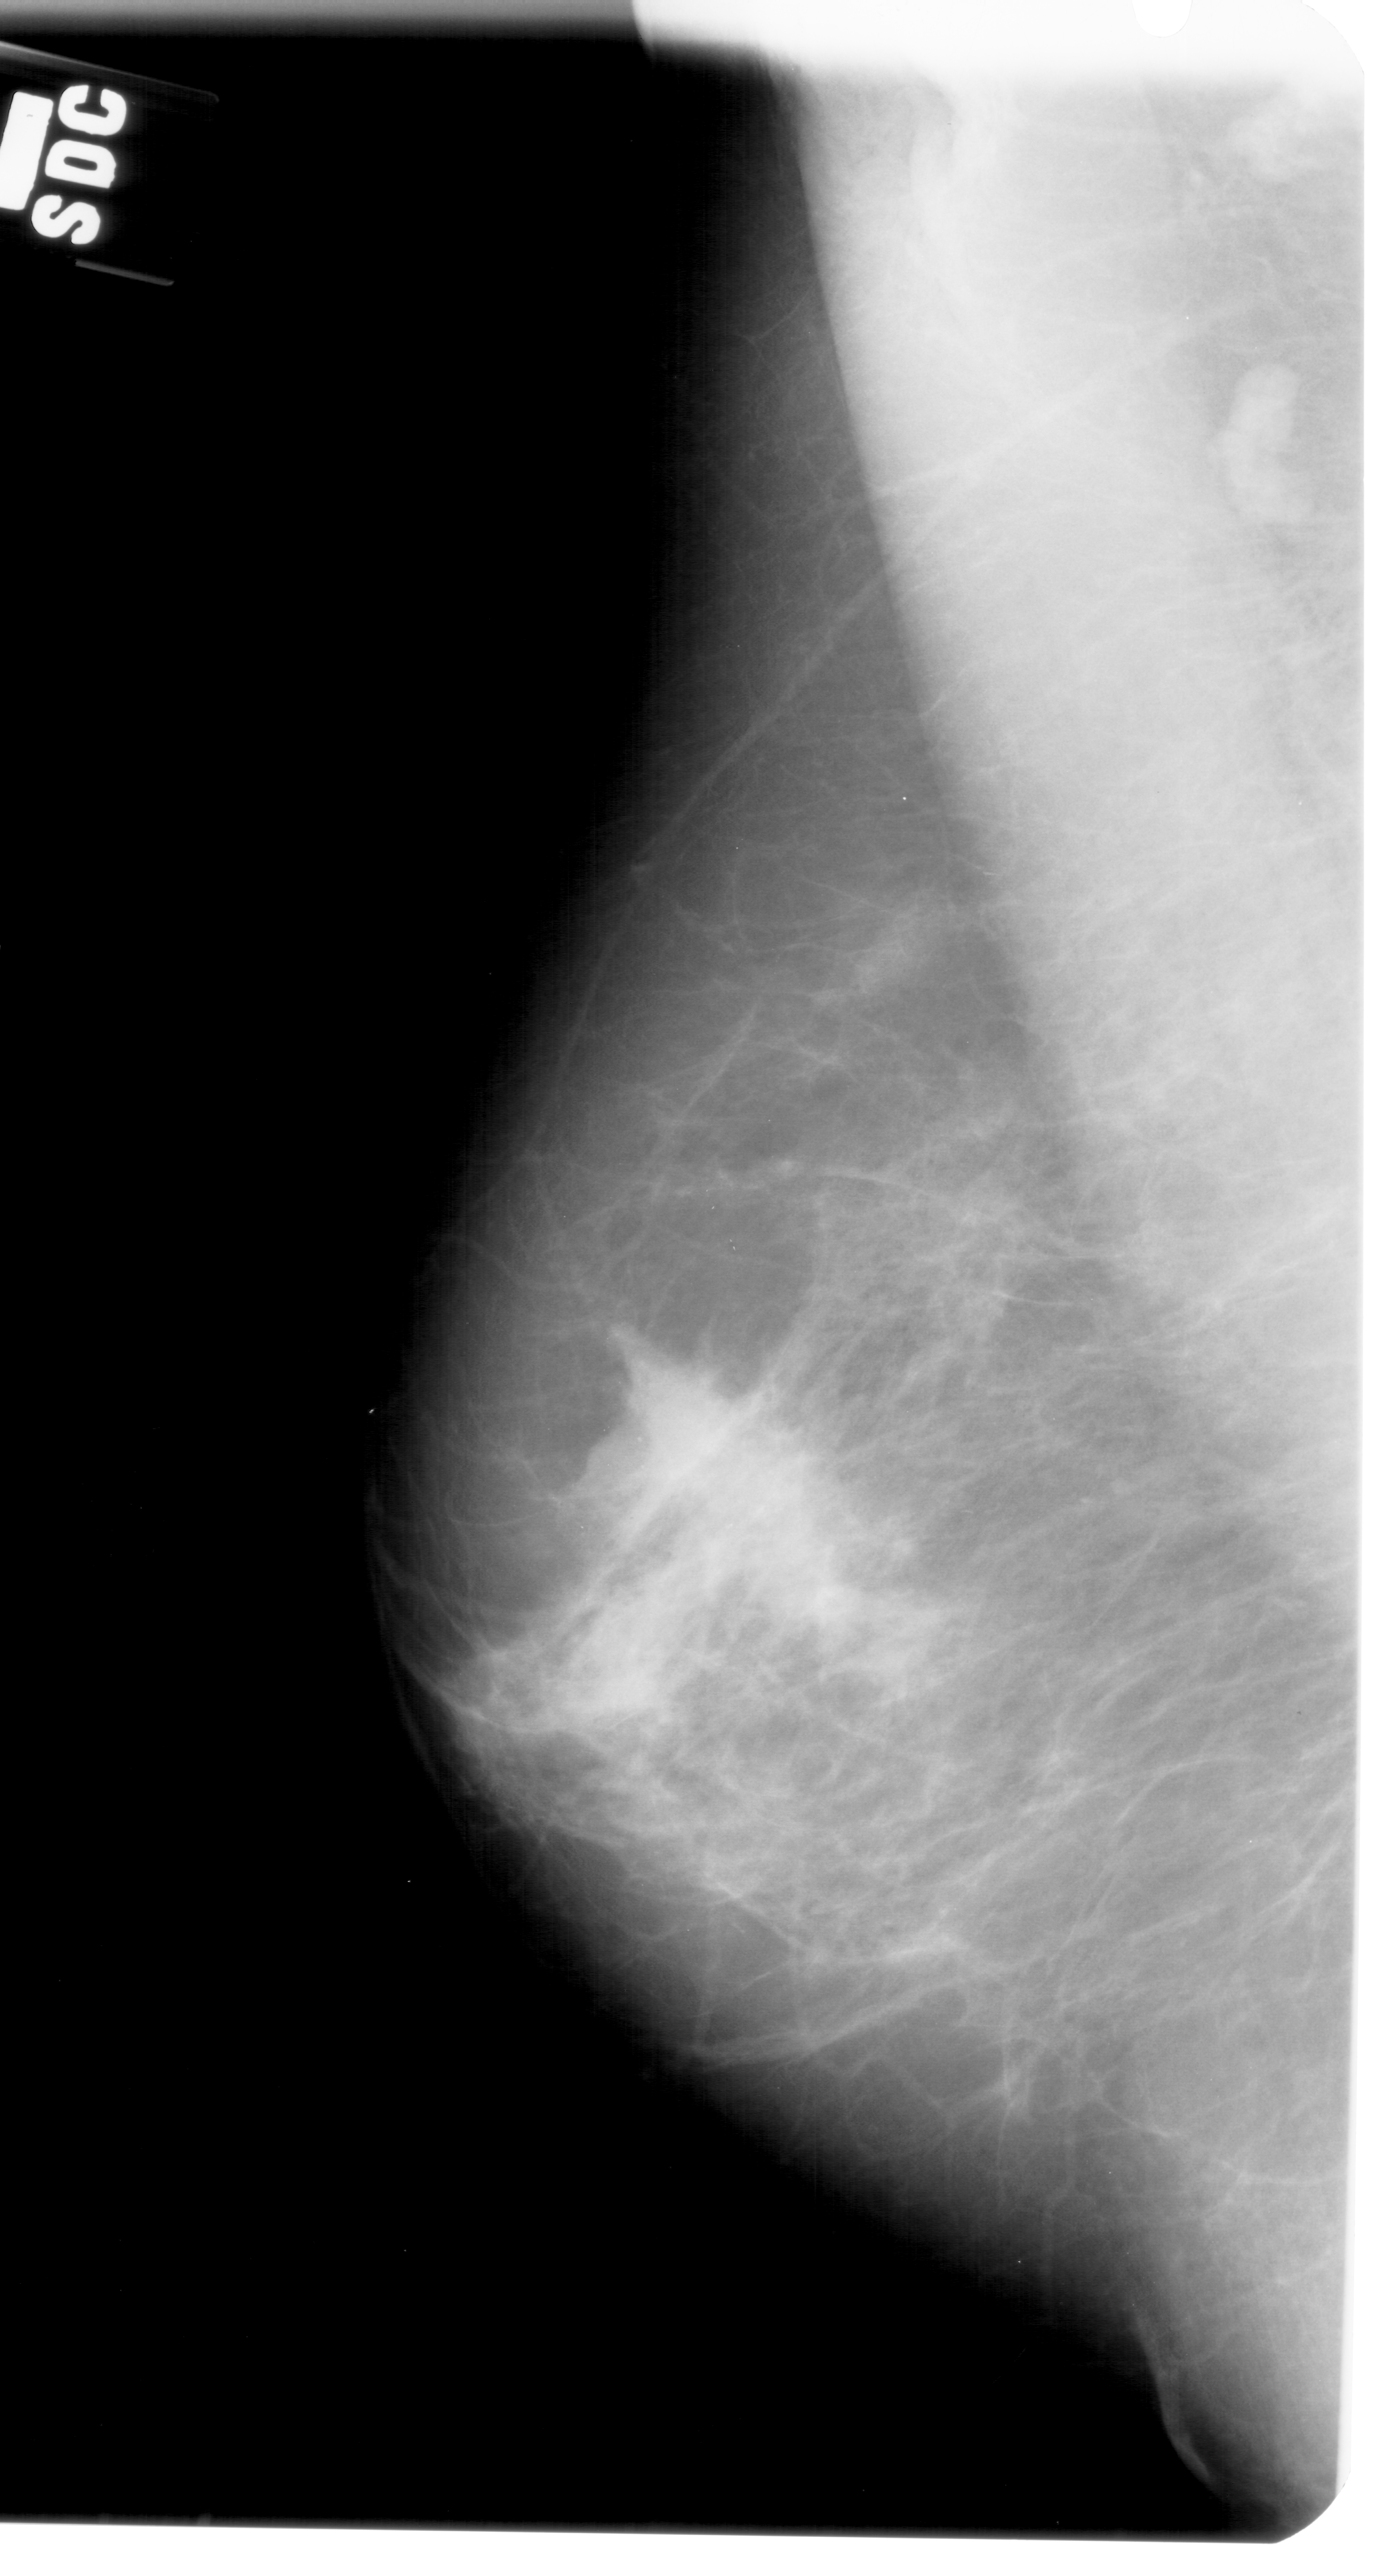
Mammogram (digitized film); left breast; MLO view; BI-RADS breast density category 2 (scale 1–4); 1380 × 2576 image matrix.
Marked abnormalities (boxes around the expert regions of interest):
- mass, shape irregular, margins ill defined; BI-RADS assessment category 4; pathology result (as recorded, not read from the image): malignant: bounding box <615,1332,870,1613> (left, top, right, bottom; pixels)